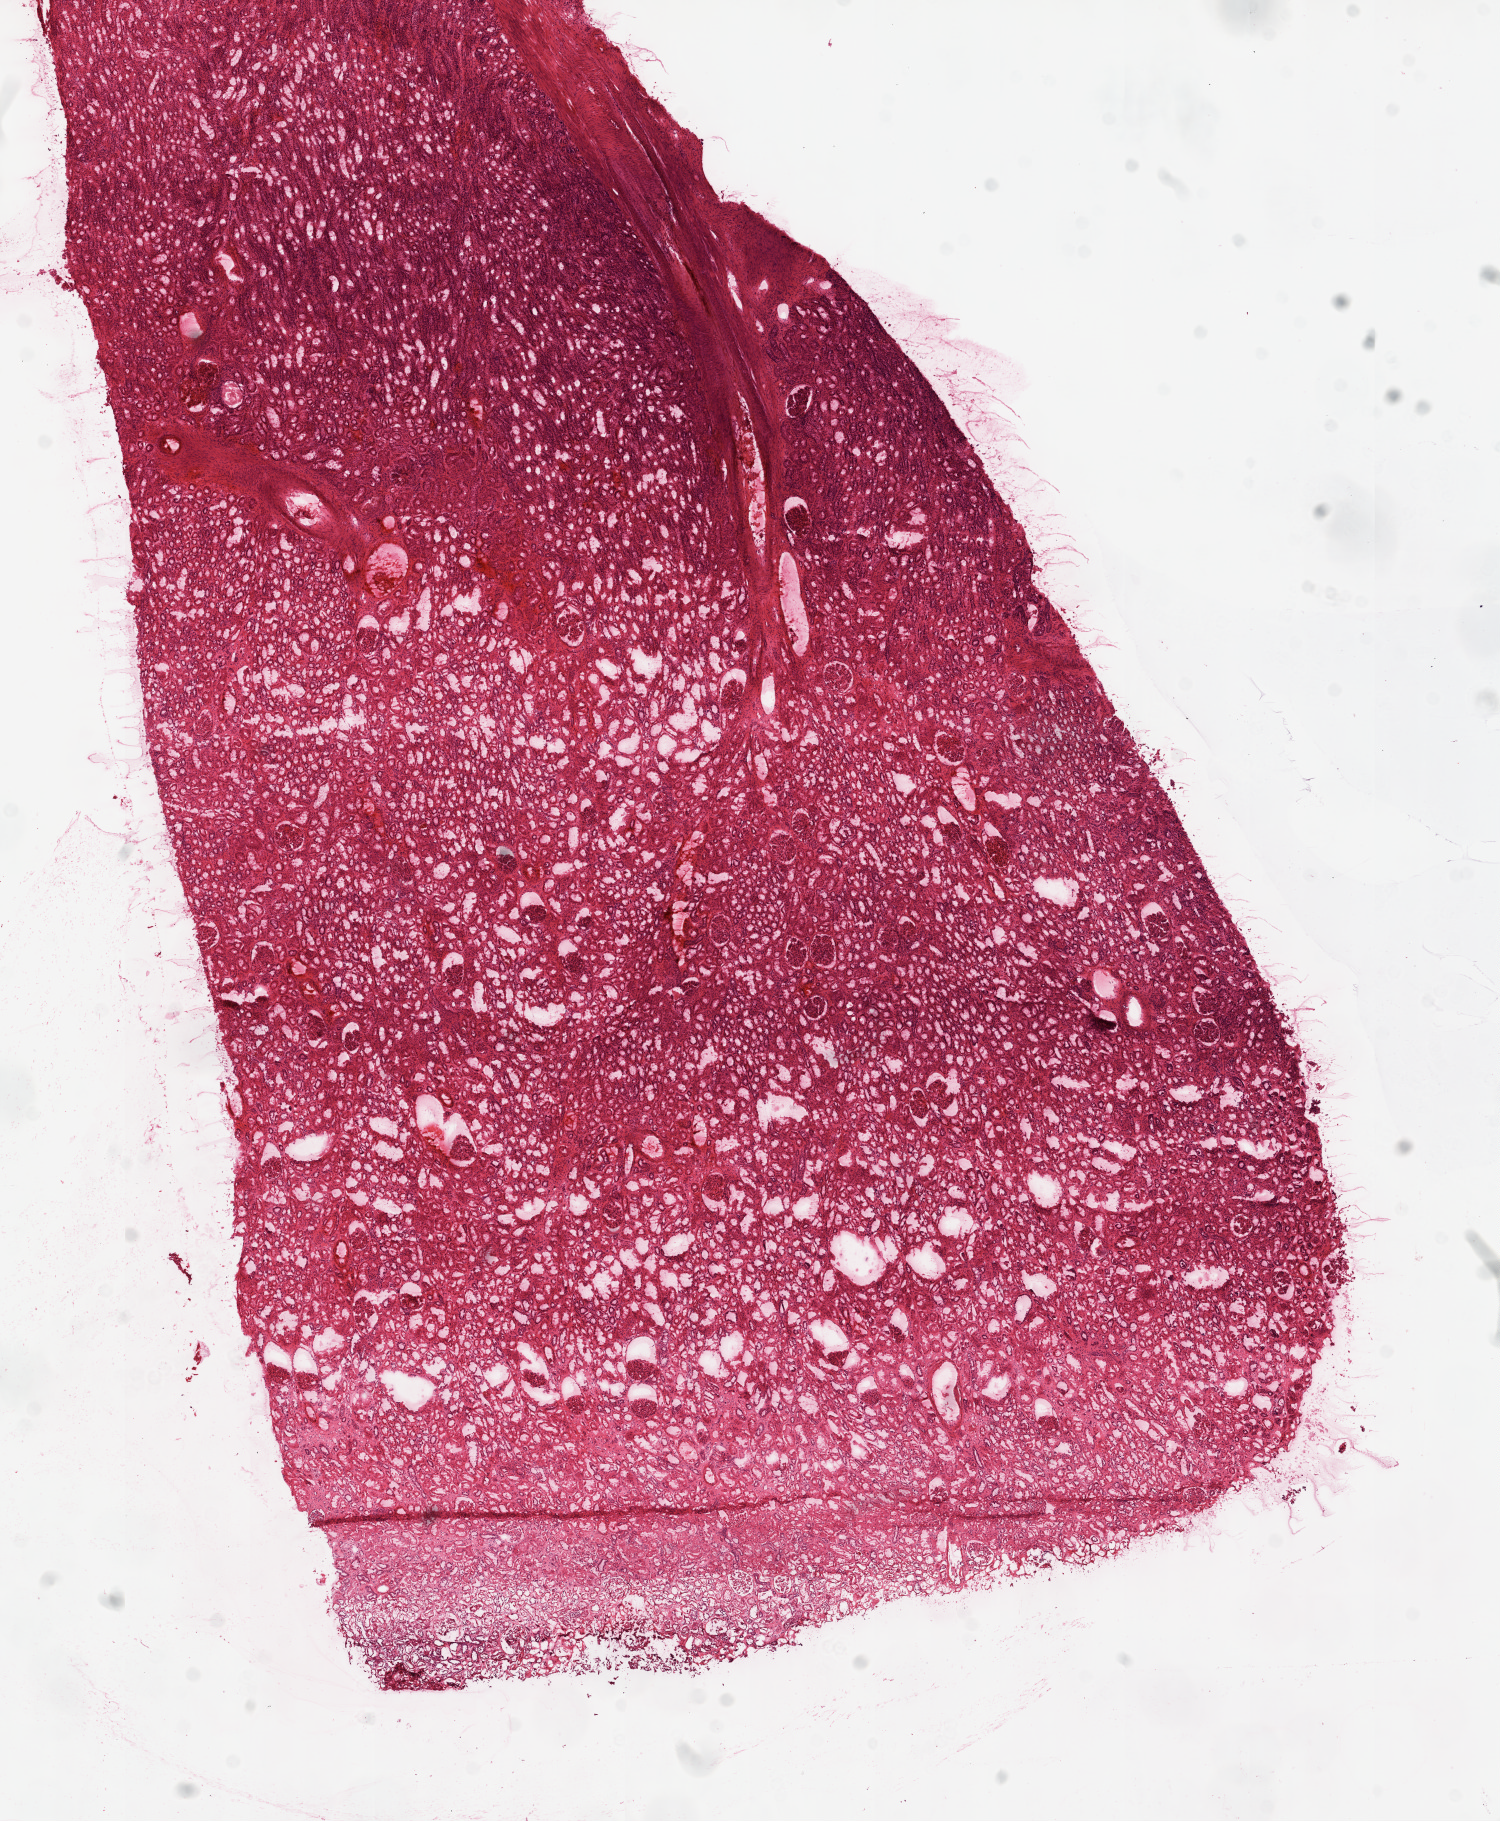
Whole-slide histology image, H&E — a low-resolution overview of the entire scanned area, about 12.0 x 14.6 mm (slide scanned at 20x), frozen section from the top of the tissue portion, kidney, solid tissue normal (non-tumour tissue) sample. Patient: male, age at initial diagnosis 58 years.
This section: solid tissue normal (non-tumour) sample from the same patient. Patient diagnosis: Clear cell adenocarcinoma, NOS.